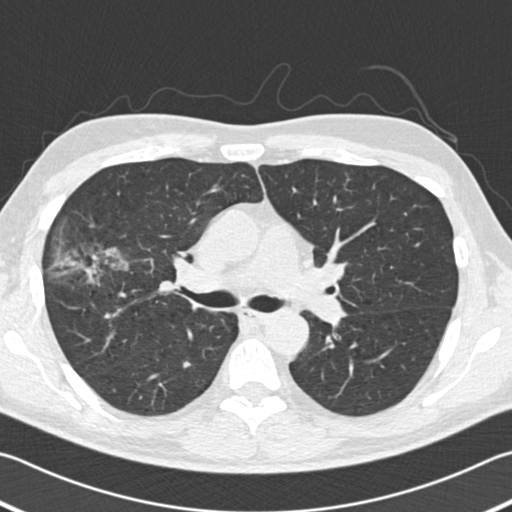
Low-dose screening chest CT, one axial slice; slice 116 of 182 in the series (ordered by position); reconstruction kernel B30f; 120 kVp; lung window (W 1500 / L -600 HU); 512 × 512 image matrix, field of view 344 × 344 mm.
Outlined on this slice (outlined manually by an expert reader):
- lesion 1 (tumor, upper lobe of right lung): bounding box [x1, y1, x2, y2] px = [50, 245, 128, 286]